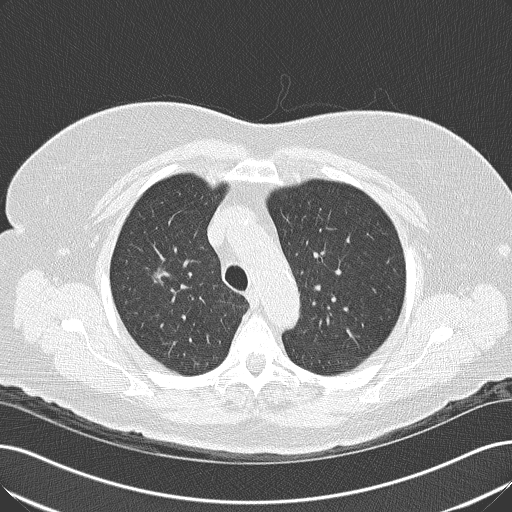
Low-dose screening chest CT, axial slice, baseline screening round, lung window (W 1500 / L -600 HU), 2 mm slice thickness, 120 kVp, slice 138 of 167 in the series. Female participant, aged 74 years at enrolment. Former smoker at enrolment.
Lesion marked by an expert reader, bounding box <136,250,194,309> (left, top, right, bottom; pixels). The screening reader recorded 2 non-calcified nodules or masses ≥4 mm on this exam (right middle lobe, right middle lobe); which of them this box marks is not recorded. Participant outcome: lung cancer diagnosed 824 days after this screen (after the third annual screen) — bronchiolo-alveolar carcinoma, non-mucinous, right upper lobe, well differentiated (G1), stage IA (AJCC 6th edition), 14 mm at pathology.